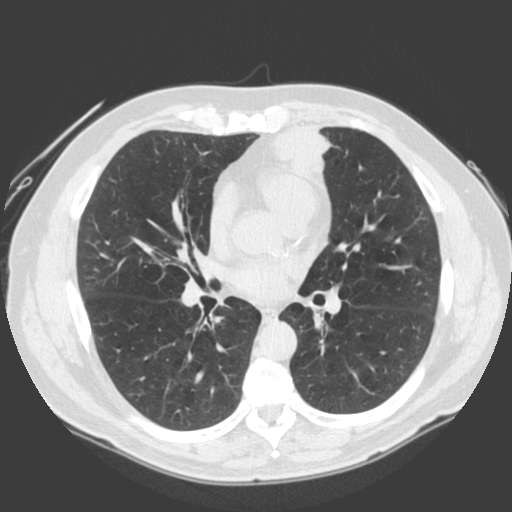
Low-dose screening chest CT, one axial slice; position 96 of 185 along the scan axis; 120 kVp; lung window (W 1500 / L -600 HU); 2 mm slice thickness; 512 × 512 image matrix.
Outlined on this slice (expert manual segmentation):
- lesion 1 (tumor, lower lobe of left lung): box from (x=275, y=128) to (x=337, y=174) px